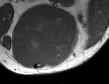
MRI of an extremity soft-tissue mass, one axial slice. Position 36 of 50 along the scan axis. MR volume resampled by the dataset authors to the PET/CT grid (not the native acquisition matrix). 109 × 84 image matrix. Male patient. Case-level facts recorded for this patient, not image findings: histological type: synovial sarcoma; site of the primary tumour: left poplietal fossa.
Annotated regions visible in this slice (expert contour drawn on MRI and transferred to this co-registered scan by the dataset authors):
- gross tumour volume (mass): bounding box [x1, y1, x2, y2] px = [25, 19, 70, 63]